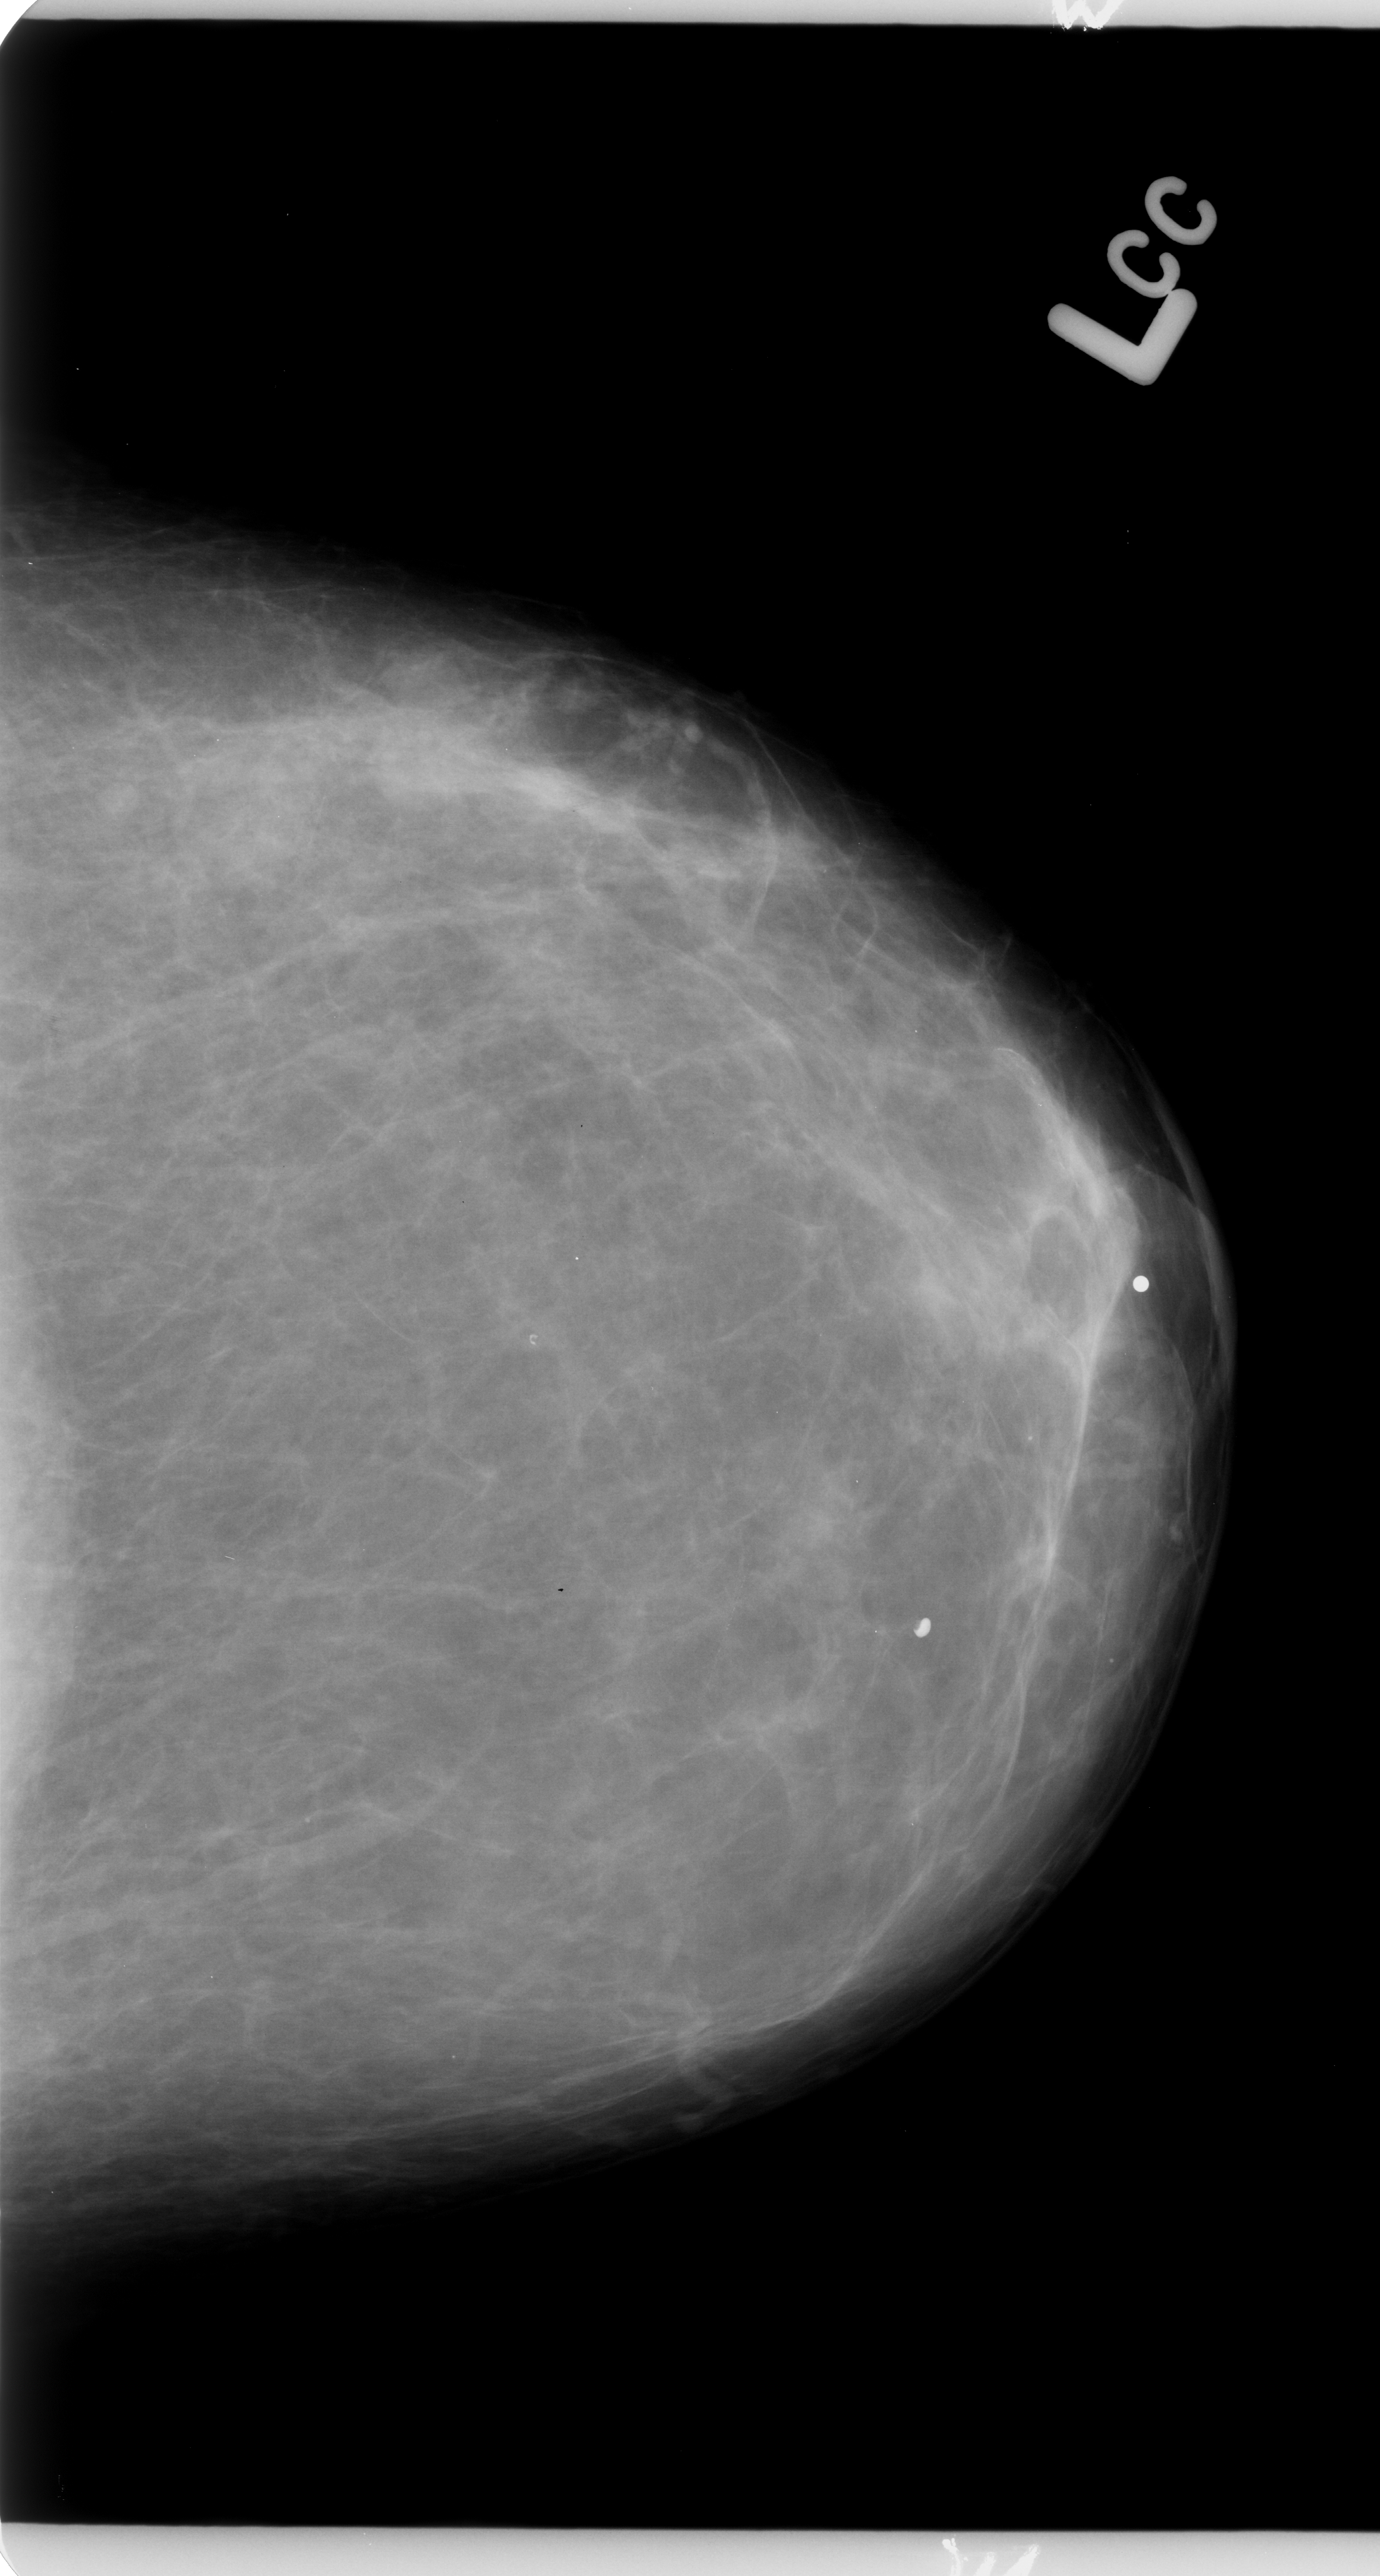
Mammogram (digitized film); left breast; CC view; BI-RADS breast density category 2 (scale 1–4).
- Finding: mass, shape irregular, margins ill defined; BI-RADS assessment category 3; pathology (as recorded): benign.